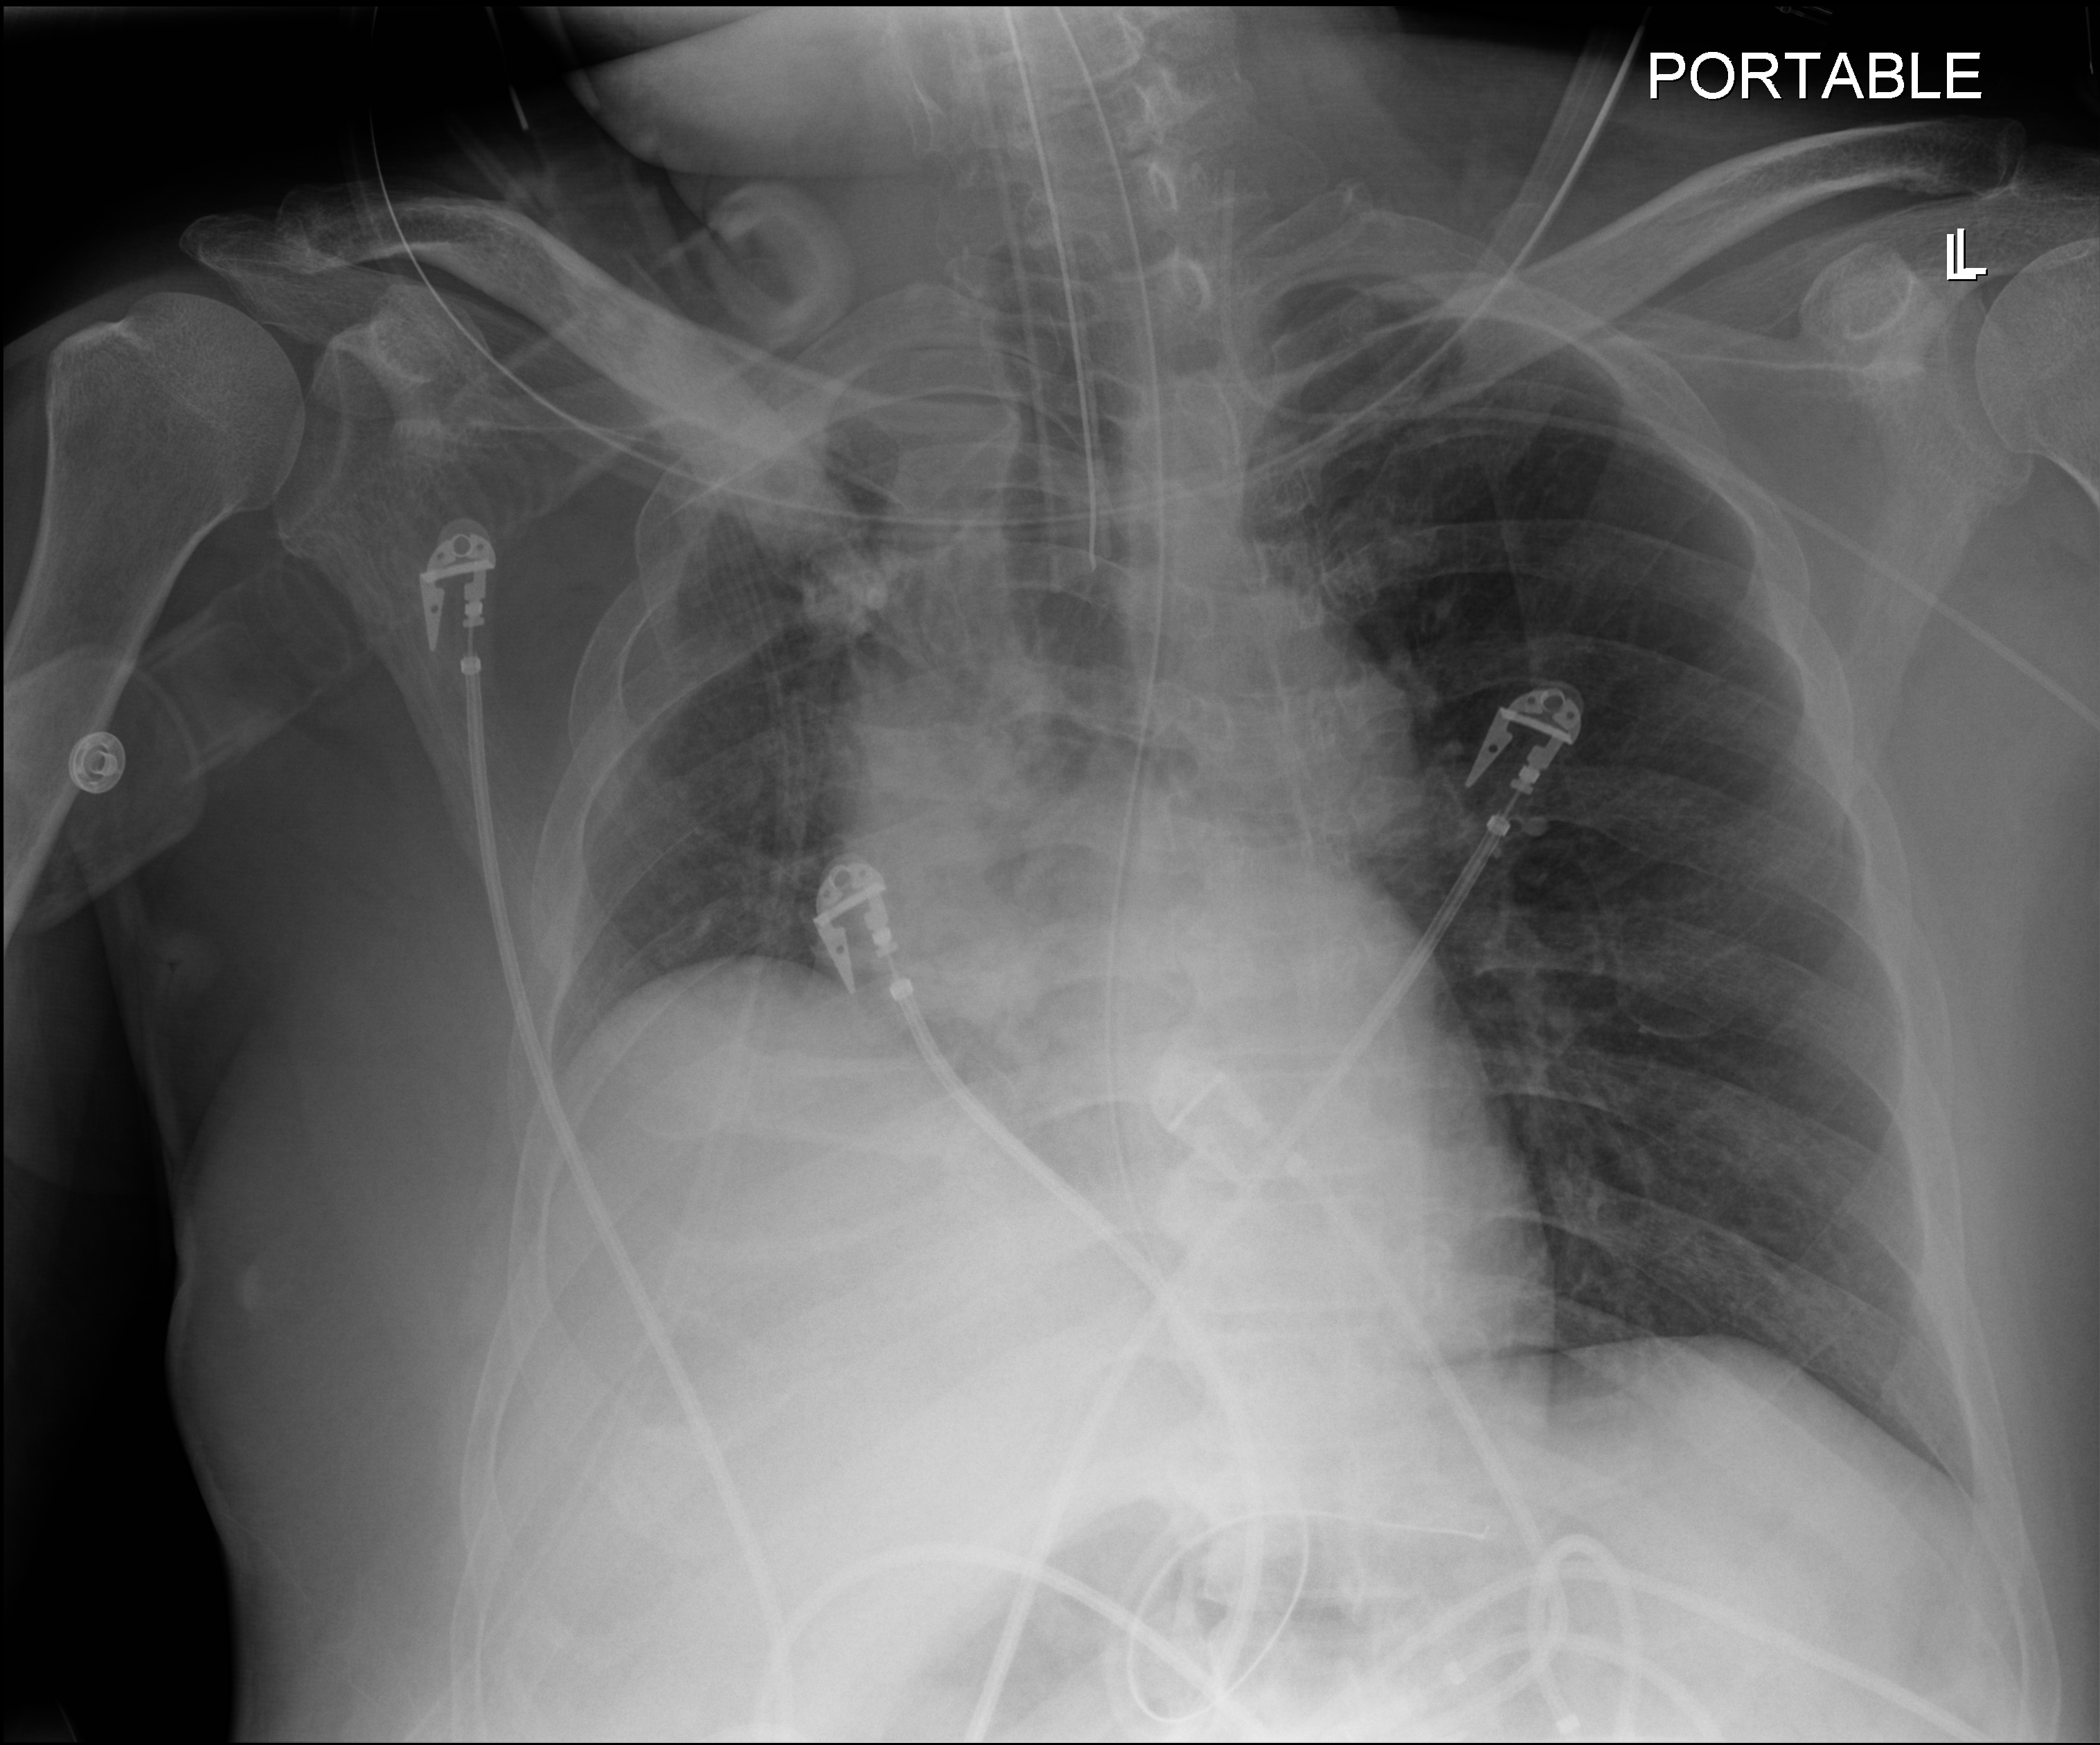
Bedside chest radiograph (digital radiography), anteroposterior (AP) projection. Patient hospitalised with COVID-19, aged 18–59 years.
Hospital-stay facts (about this admission, not read from this image; timing relative to this image not recorded):
- hypertension (admission record): no